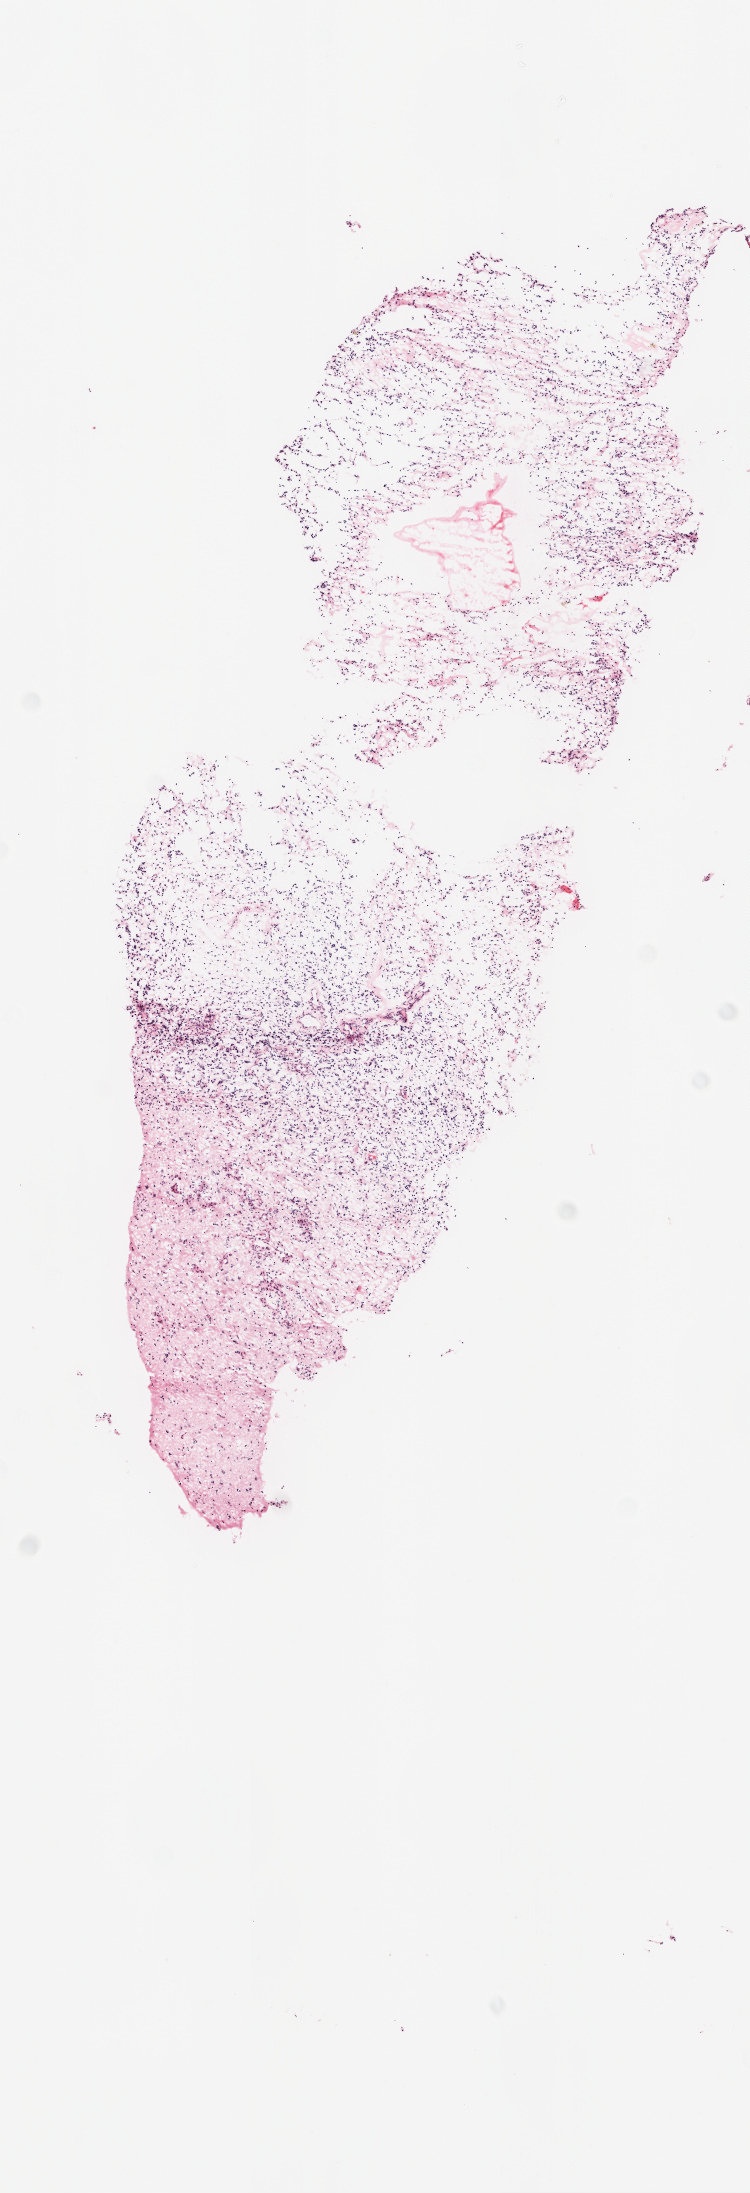
Whole-slide histology image, H&E, shown as a low-resolution overview of the whole scanned area (about 3.0 x 8.8 mm), frozen section from the top of the tissue portion, sample: primary tumour, brain. Patient: male, age at initial diagnosis 61 years. Slide review estimates, as recorded: tumour cells 70%, tumour nuclei 100%, normal cells 10%, stromal cells 20%, necrosis 0%.
Pathologic diagnosis: Glioblastoma.